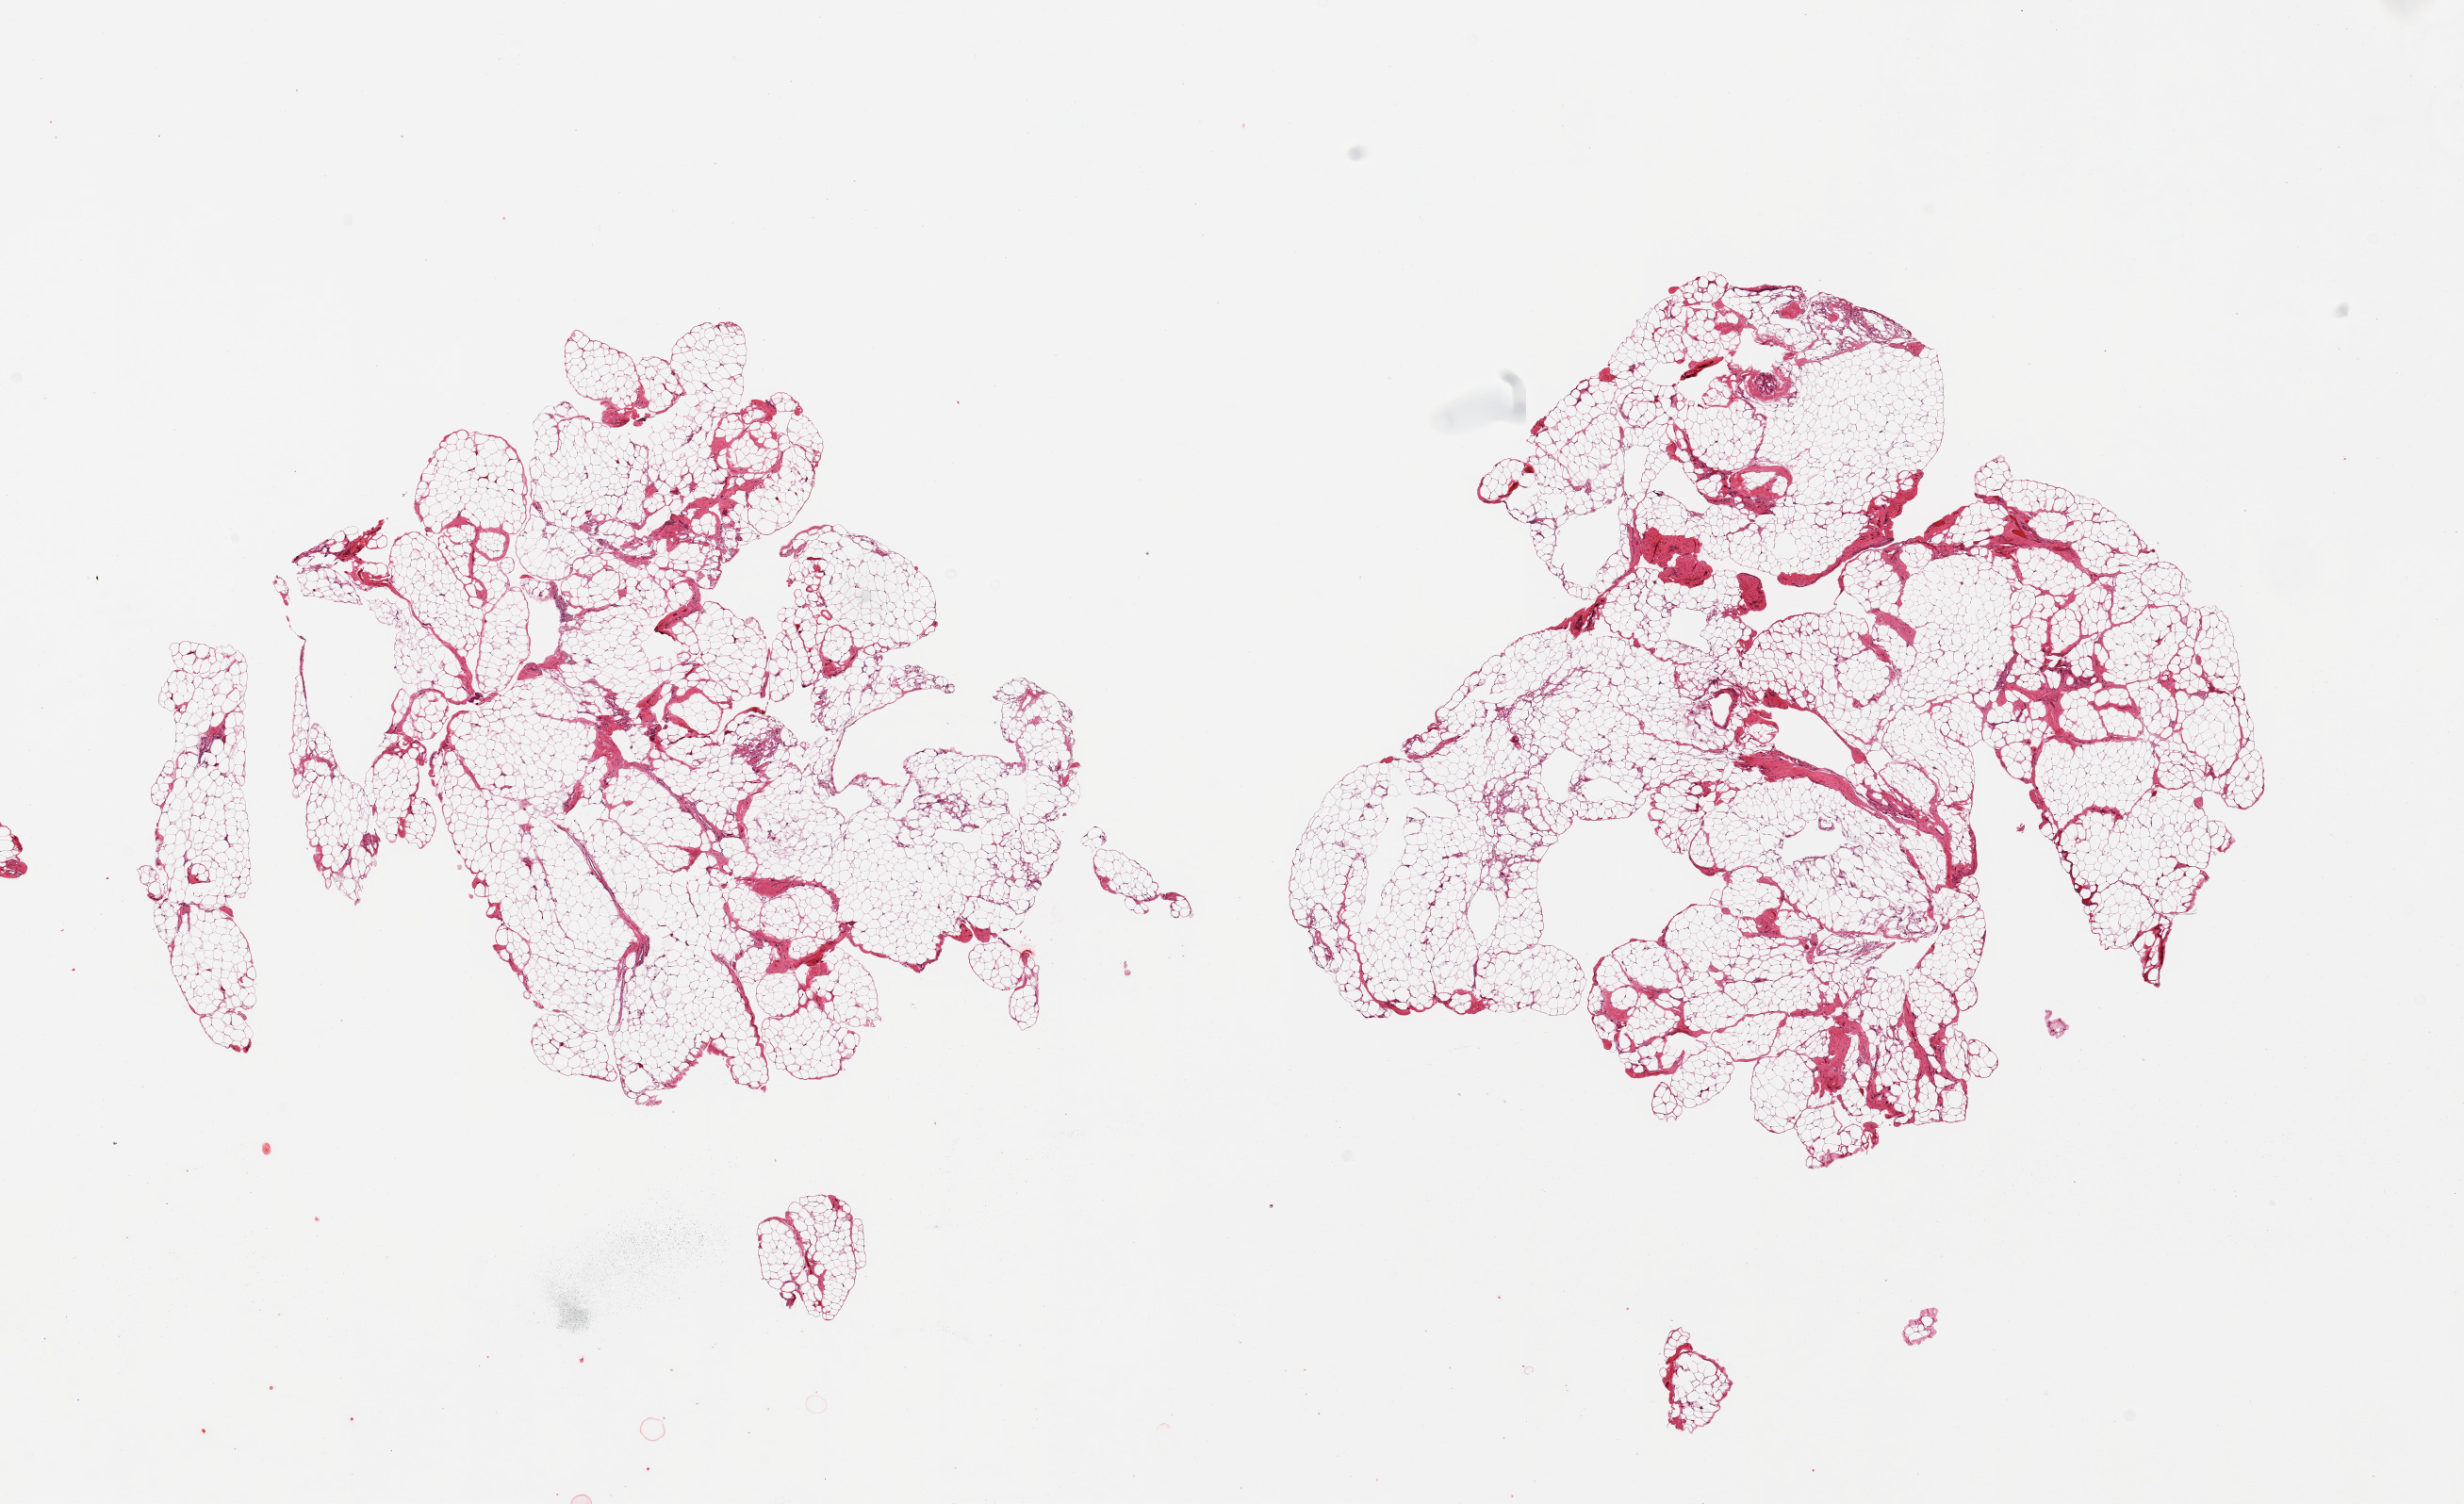
H&E whole-slide image, shown as a low-resolution overview of the whole scanned area (about 20.7 x 12.6 mm, from a 20x scan); PAXgene-fixed, paraffin-embedded tissue; sampled site (target tissue): omentum; donor tissue sample. Male donor.
Reviewer comment on this tissue sample: 2 pieces, fascia is ~10% tissue.